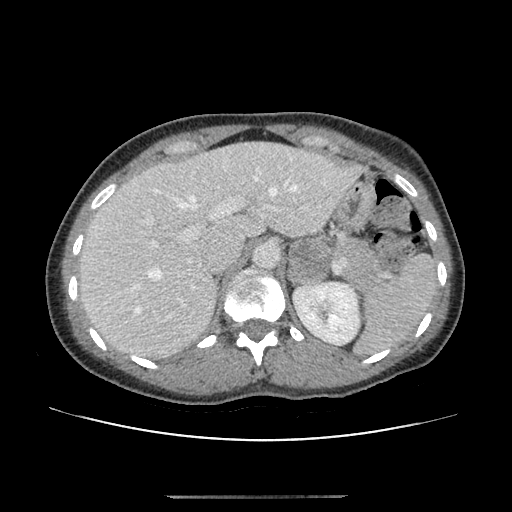
Contrast-enhanced abdominal CT, one axial slice. Slice 74 of 179 in the series (ordered by position). 120 kVp. Soft-tissue window (W 400 / L 40 HU). 2.5 mm slice thickness. 512 × 512 image matrix, field of view 360 × 360 mm. Patient: female, 51 years. From the clinical record (not read from this slice): diagnosis: adrenocortical carcinoma; tumour side: left adrenal.
Annotated regions visible in this slice (semi-automatically segmented with operator editing):
- mass: bounding box (x1, y1, x2, y2) in pixels: (288, 239, 330, 283)